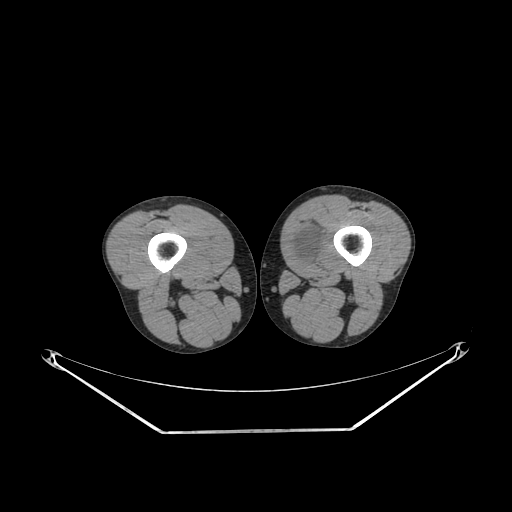
CT of an extremity soft-tissue mass (from a PET/CT study), one axial slice; reconstruction kernel SOFT; 140 kVp; soft-tissue window (W 400 / L 40 HU); 3.75 mm slice thickness; 512 × 512 image matrix, field of view 500 × 500 mm. Male patient. From the clinical record (not read from this slice): histological type: mixoid liposarcoma; grade: low; site of the primary tumour: left thigh.
Annotated regions visible in this slice (expert contour drawn on MRI and transferred to this co-registered scan by the dataset authors):
- gross tumour volume (mass): bounding box (x1, y1, x2, y2) in pixels: (288, 228, 323, 266)